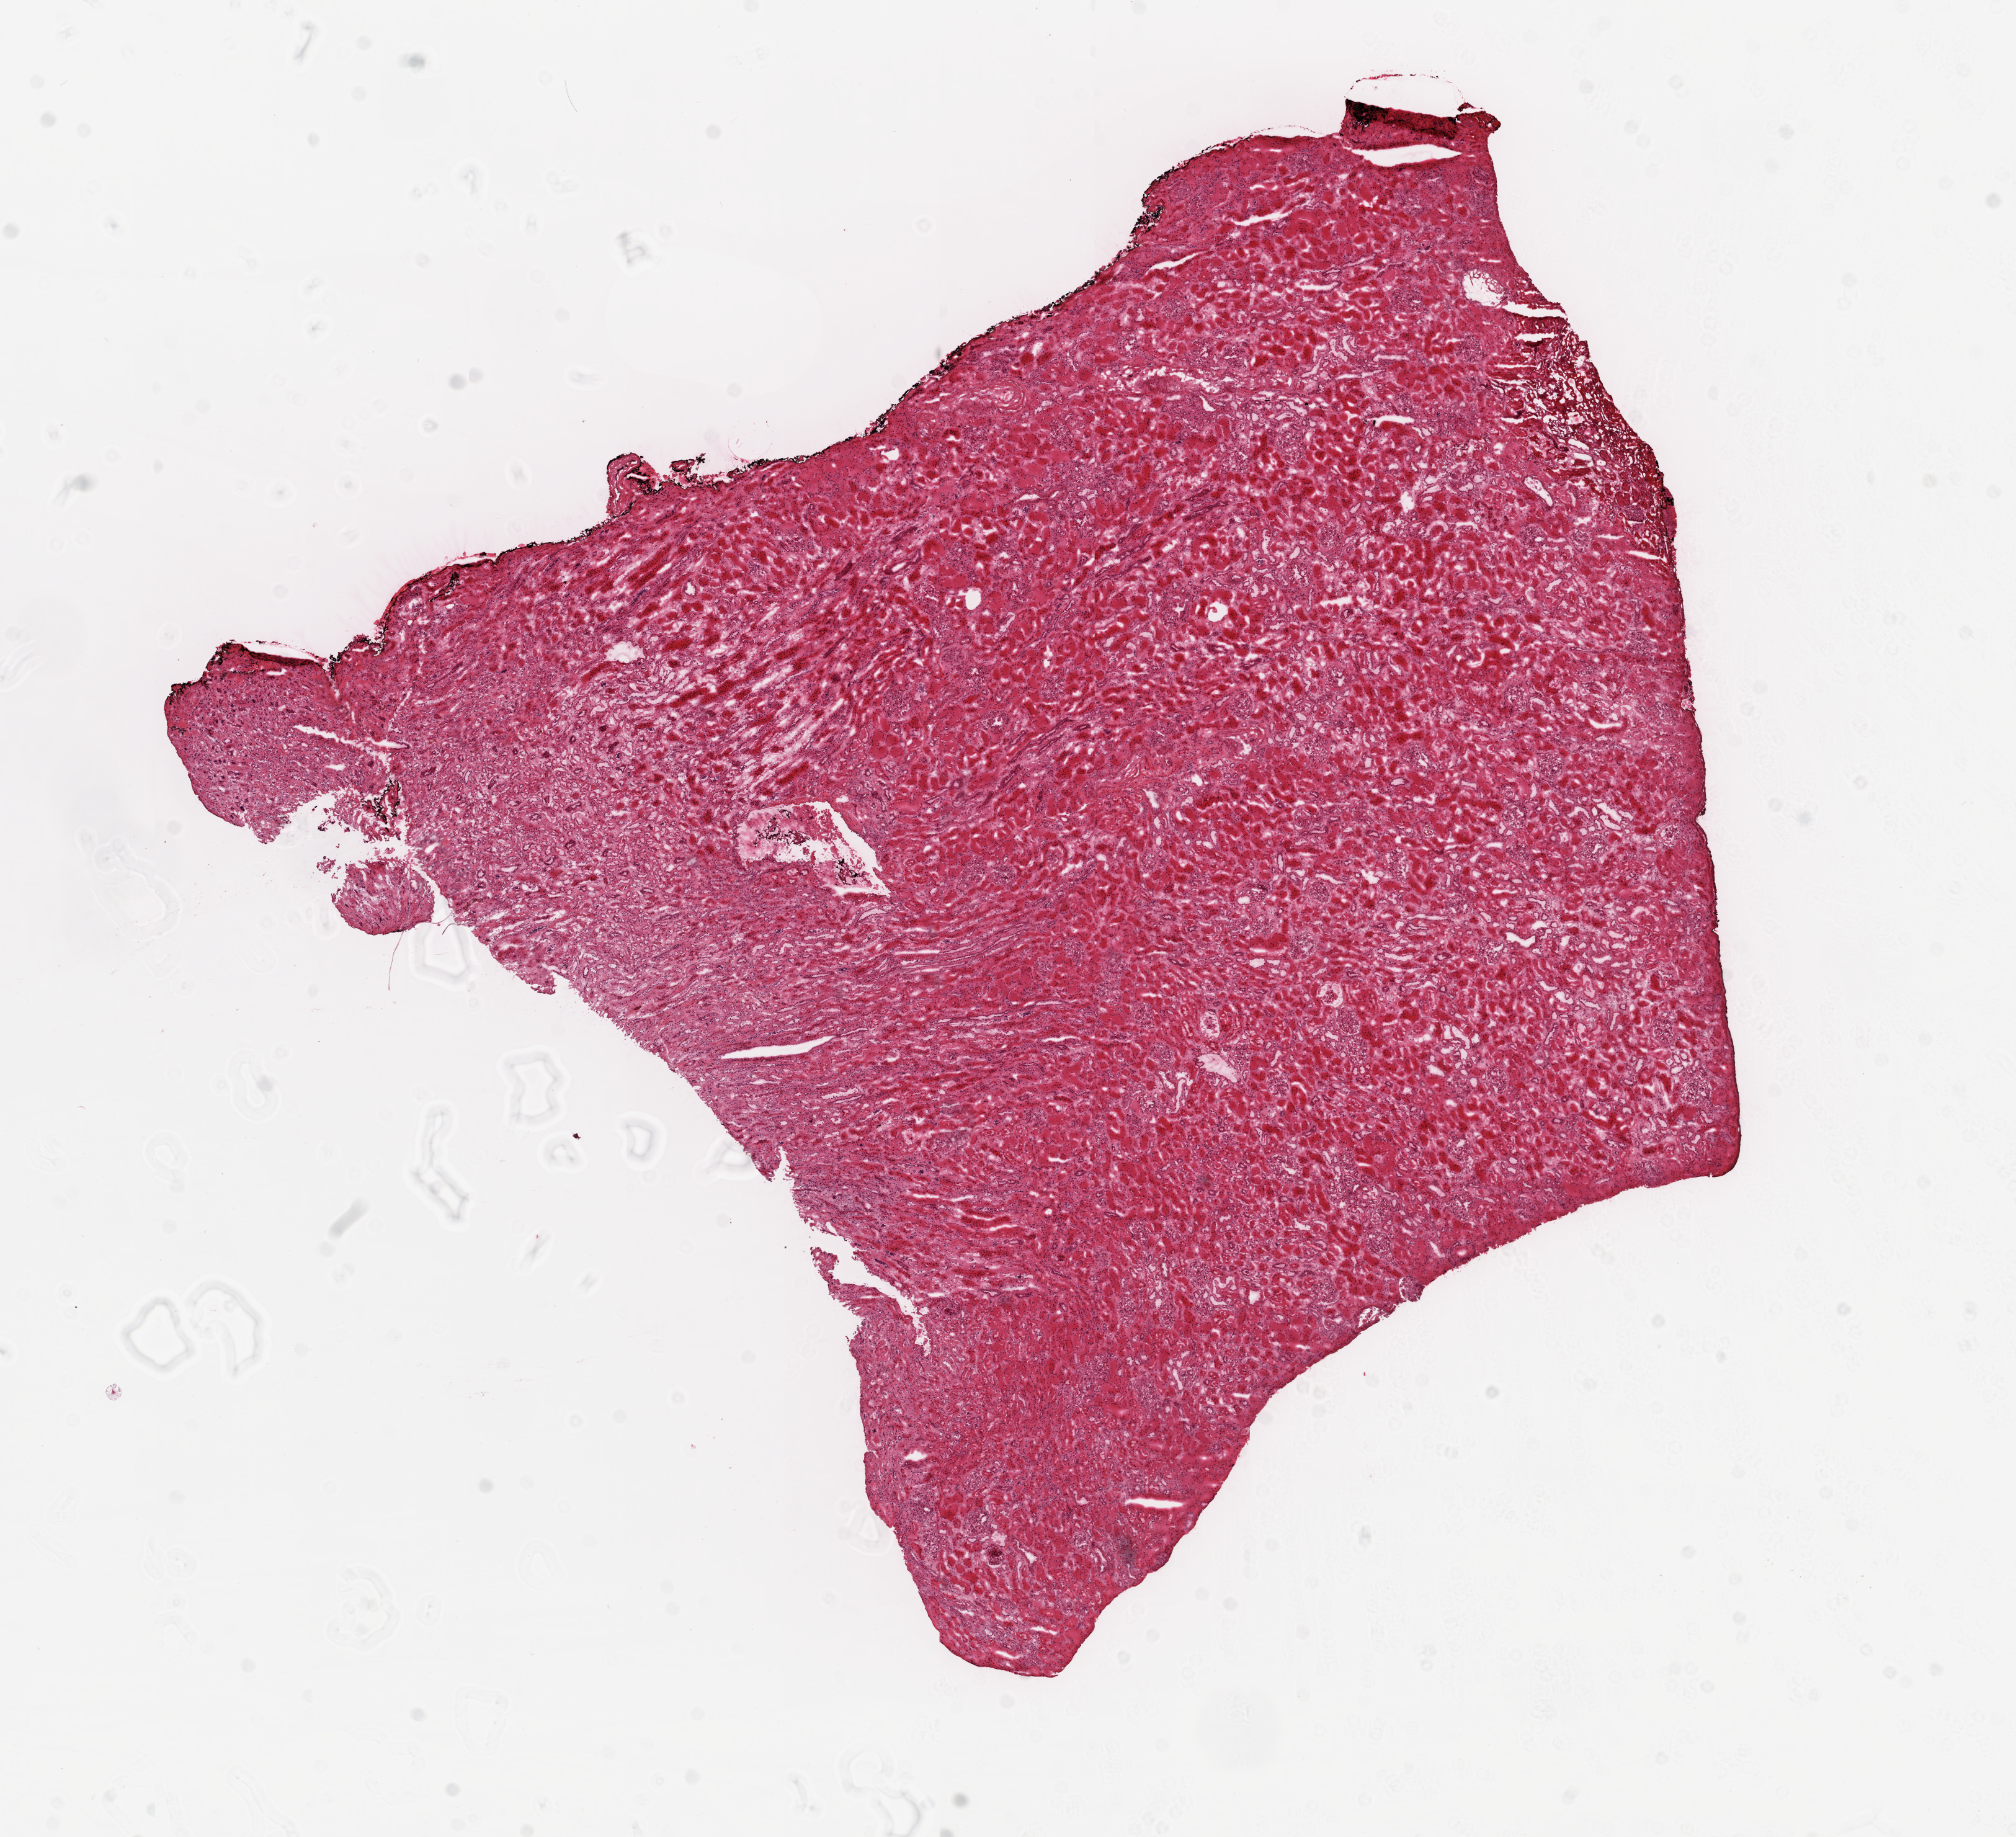
Digitized H&E tissue section (whole slide), shown as a low-resolution overview of the whole scanned area (about 13.0 x 11.9 mm); frozen section from the top of the tissue portion; sample: solid tissue normal (non-tumour tissue), kidney. Male patient; age at initial diagnosis 53 years.
This section: solid tissue normal sample (biorepository sample class). Patient diagnosis: Clear cell adenocarcinoma, NOS.